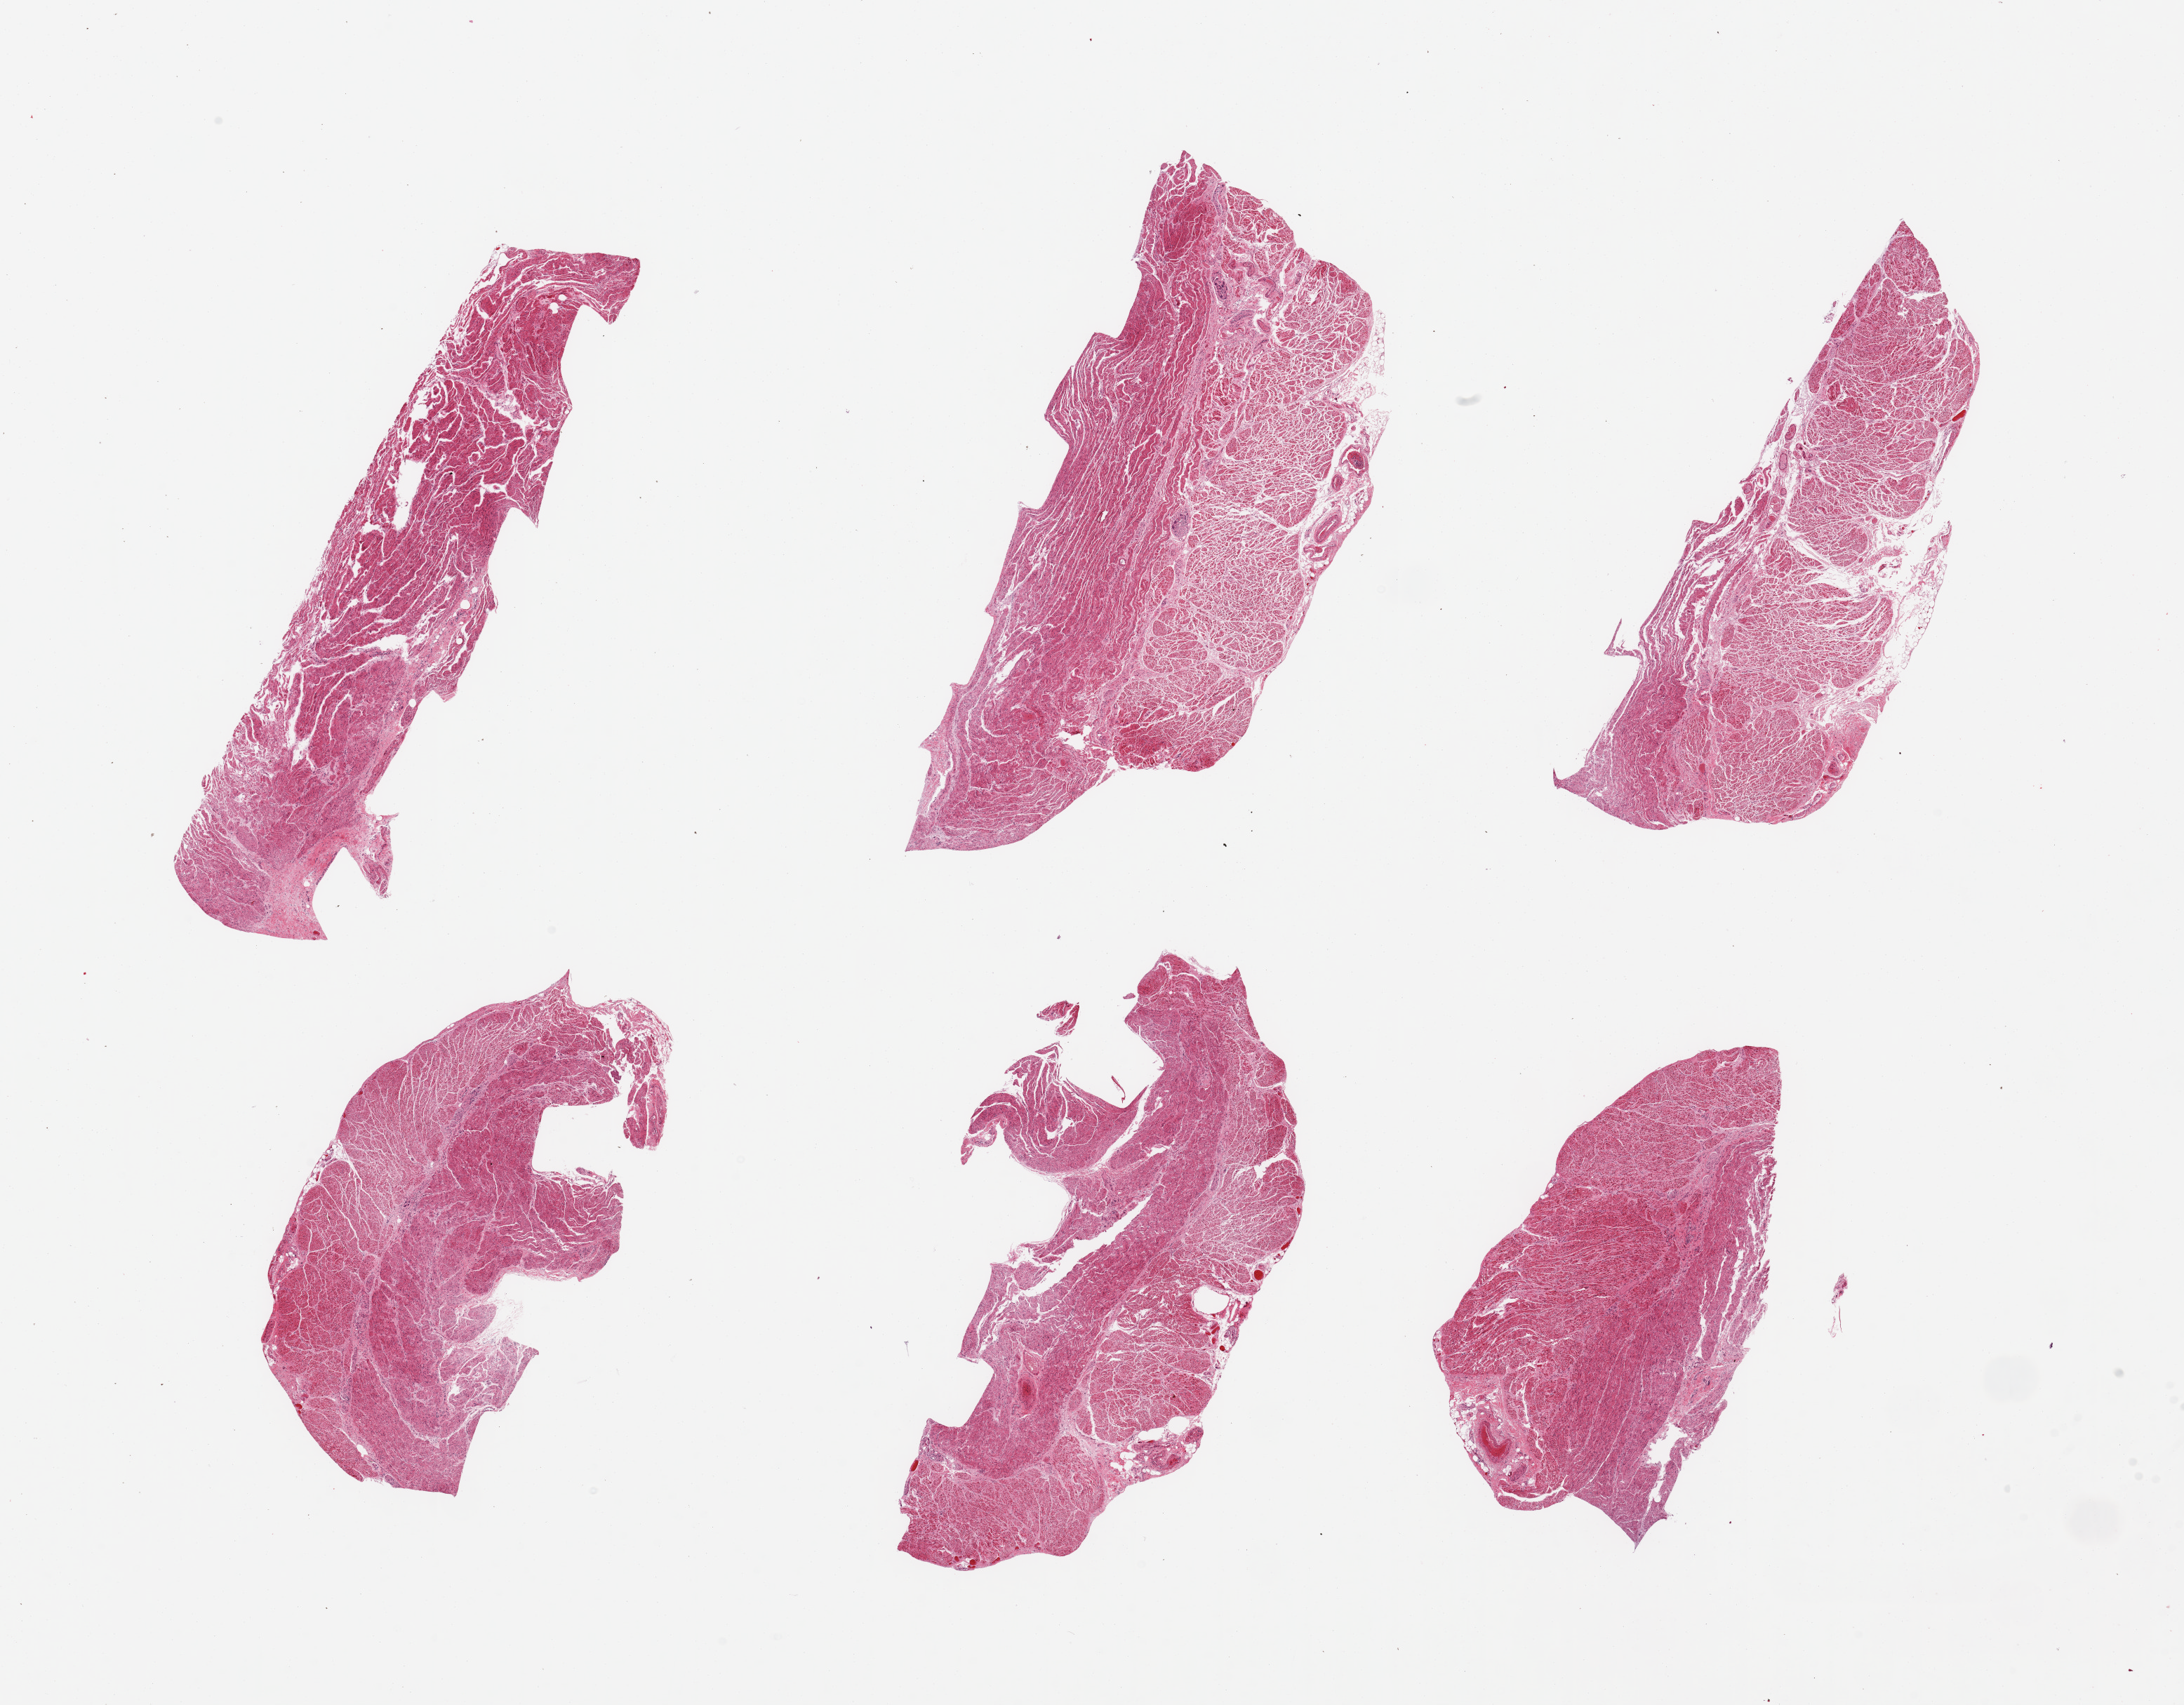
Whole-slide image, haematoxylin and eosin stain — shown as a low-resolution overview of the whole scanned area (about 24.6 x 19.2 mm, from a 20x scan). PAXgene-fixed, paraffin-embedded tissue. Target tissue: gastroesophageal junction. Donor tissue sample.
Reviewer comment on this tissue sample: 6 pieces; muscularis.